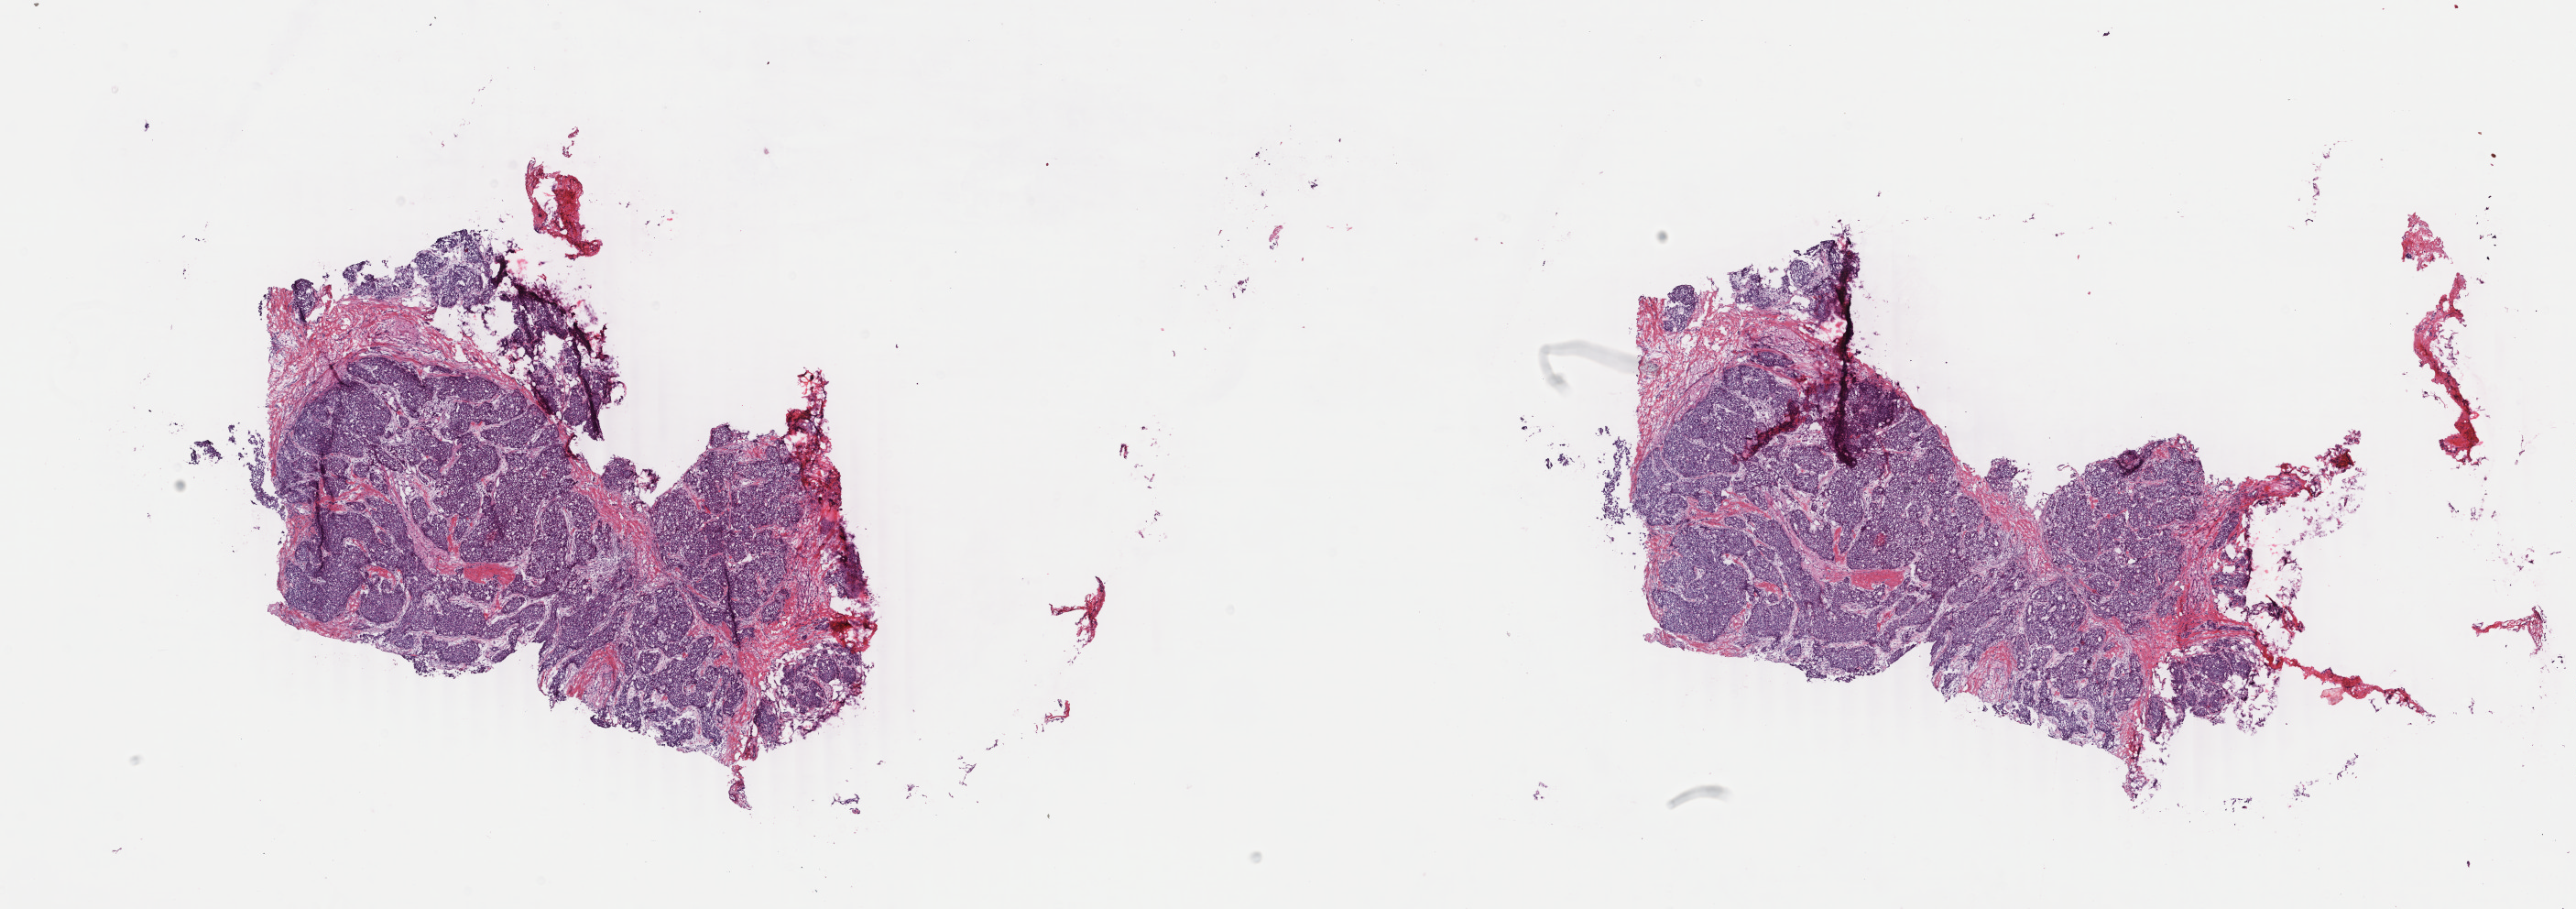
Digitized H&E-stained tissue section (whole slide) — a low-resolution overview of the entire scanned area, about 22.4 x 7.9 mm (slide scanned at 40x). Frozen section from the bottom of the tissue portion. Breast, primary tumour sample. Female, age 37 years at initial diagnosis. Composition of this section per pathologist review: tumour cells 74%, tumour nuclei 90%, normal cells 15%, stromal cells 10%, necrosis 1%. Infiltration values recorded for this section: lymphocyte infiltration 4%, monocyte infiltration 0%, neutrophil infiltration 0%.
* histologic diagnosis: Infiltrating duct carcinoma, NOS
* AJCC pathologic stage: IIA
* lymph nodes positive (case pathology): 0 of 1 examined